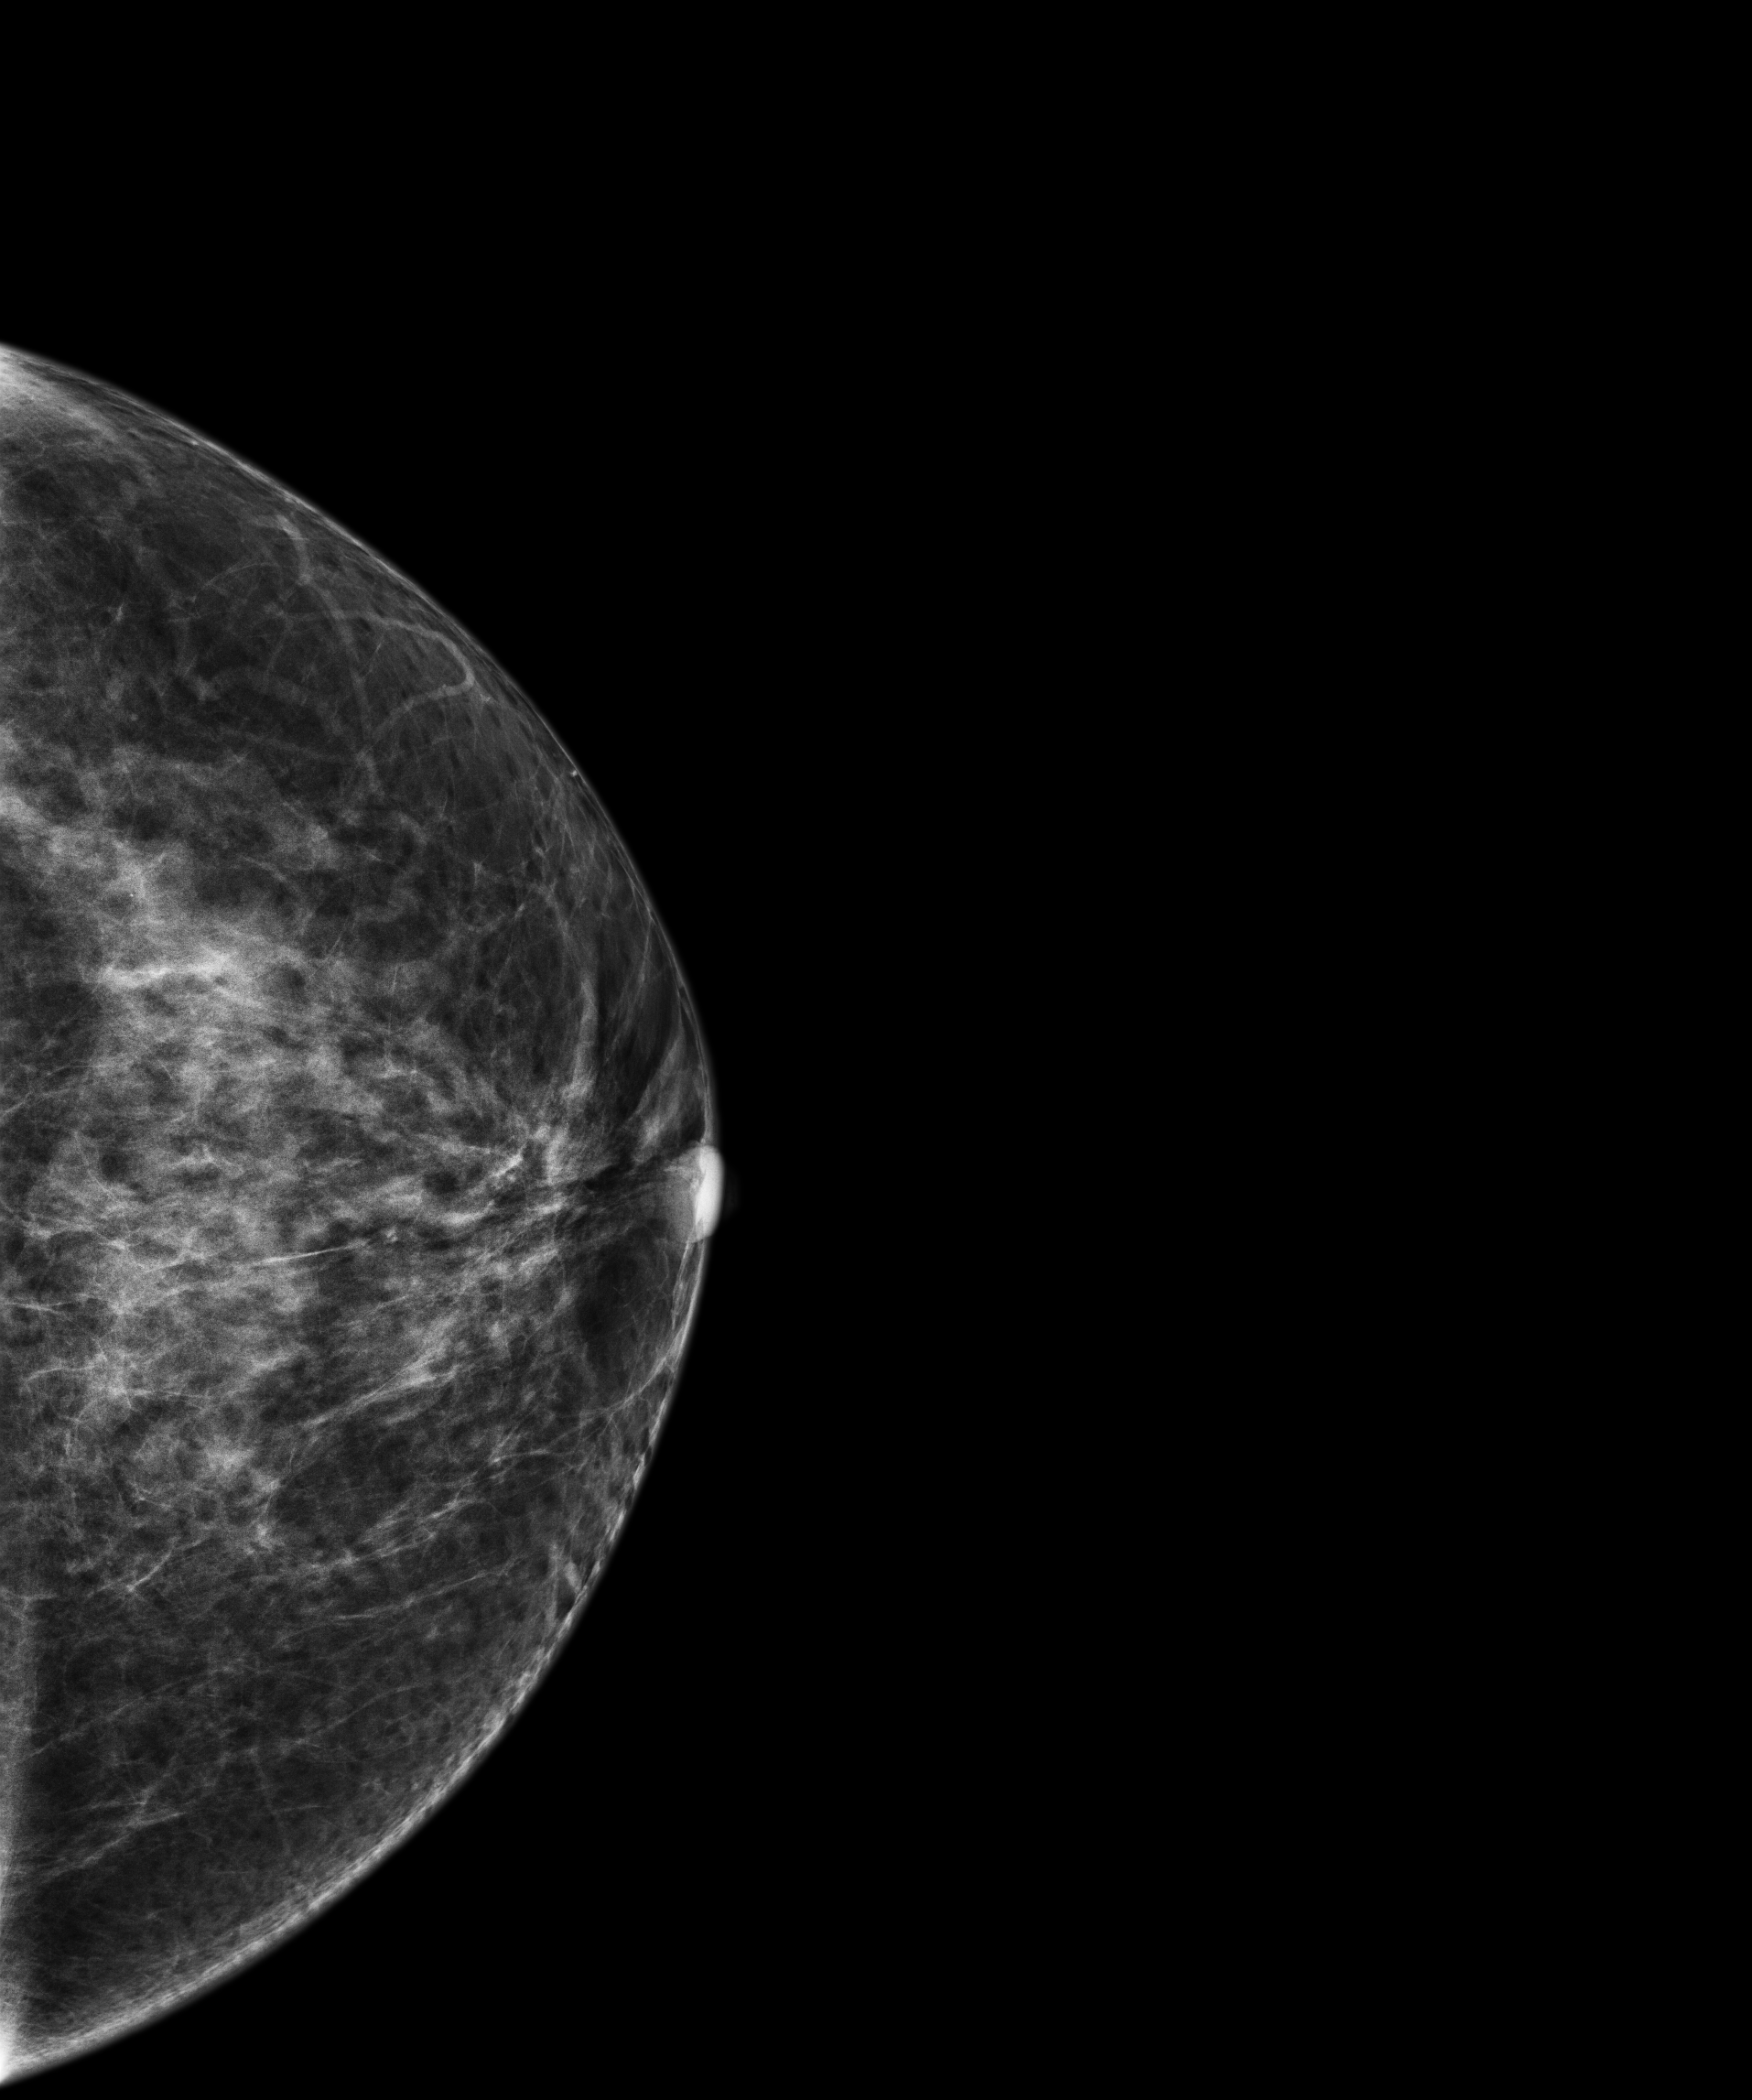
Annual screening mammography examination; compressed breast thickness 58.8 mm. Patient aged 49 years (female).
Image type: full-field digital mammogram. Breast: left. Projection: cranio-caudal projection.